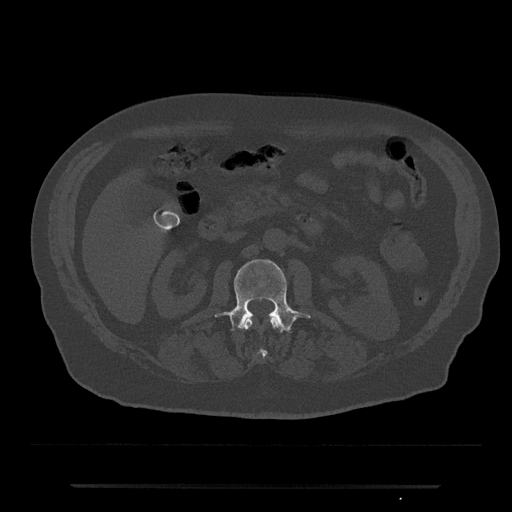
CT including the spine, one axial slice. Position 487 of 797 along the scan axis. 120 kVp. Bone window (W 1800 / L 400 HU). 512 × 512 image matrix, field of view 434 × 434 mm. Patient: male, 80 years. Case-level facts recorded for this patient, not image findings: primary cancer: prostate; vertebrae with lytic lesions (as recorded): L1, T11.
Structures marked on this image (semi-automatically segmented with operator editing):
- L1 vertebra: bounding box (x1, y1, x2, y2) in pixels: (242, 317, 281, 357)
- L2 vertebra: (215, 259, 311, 332)